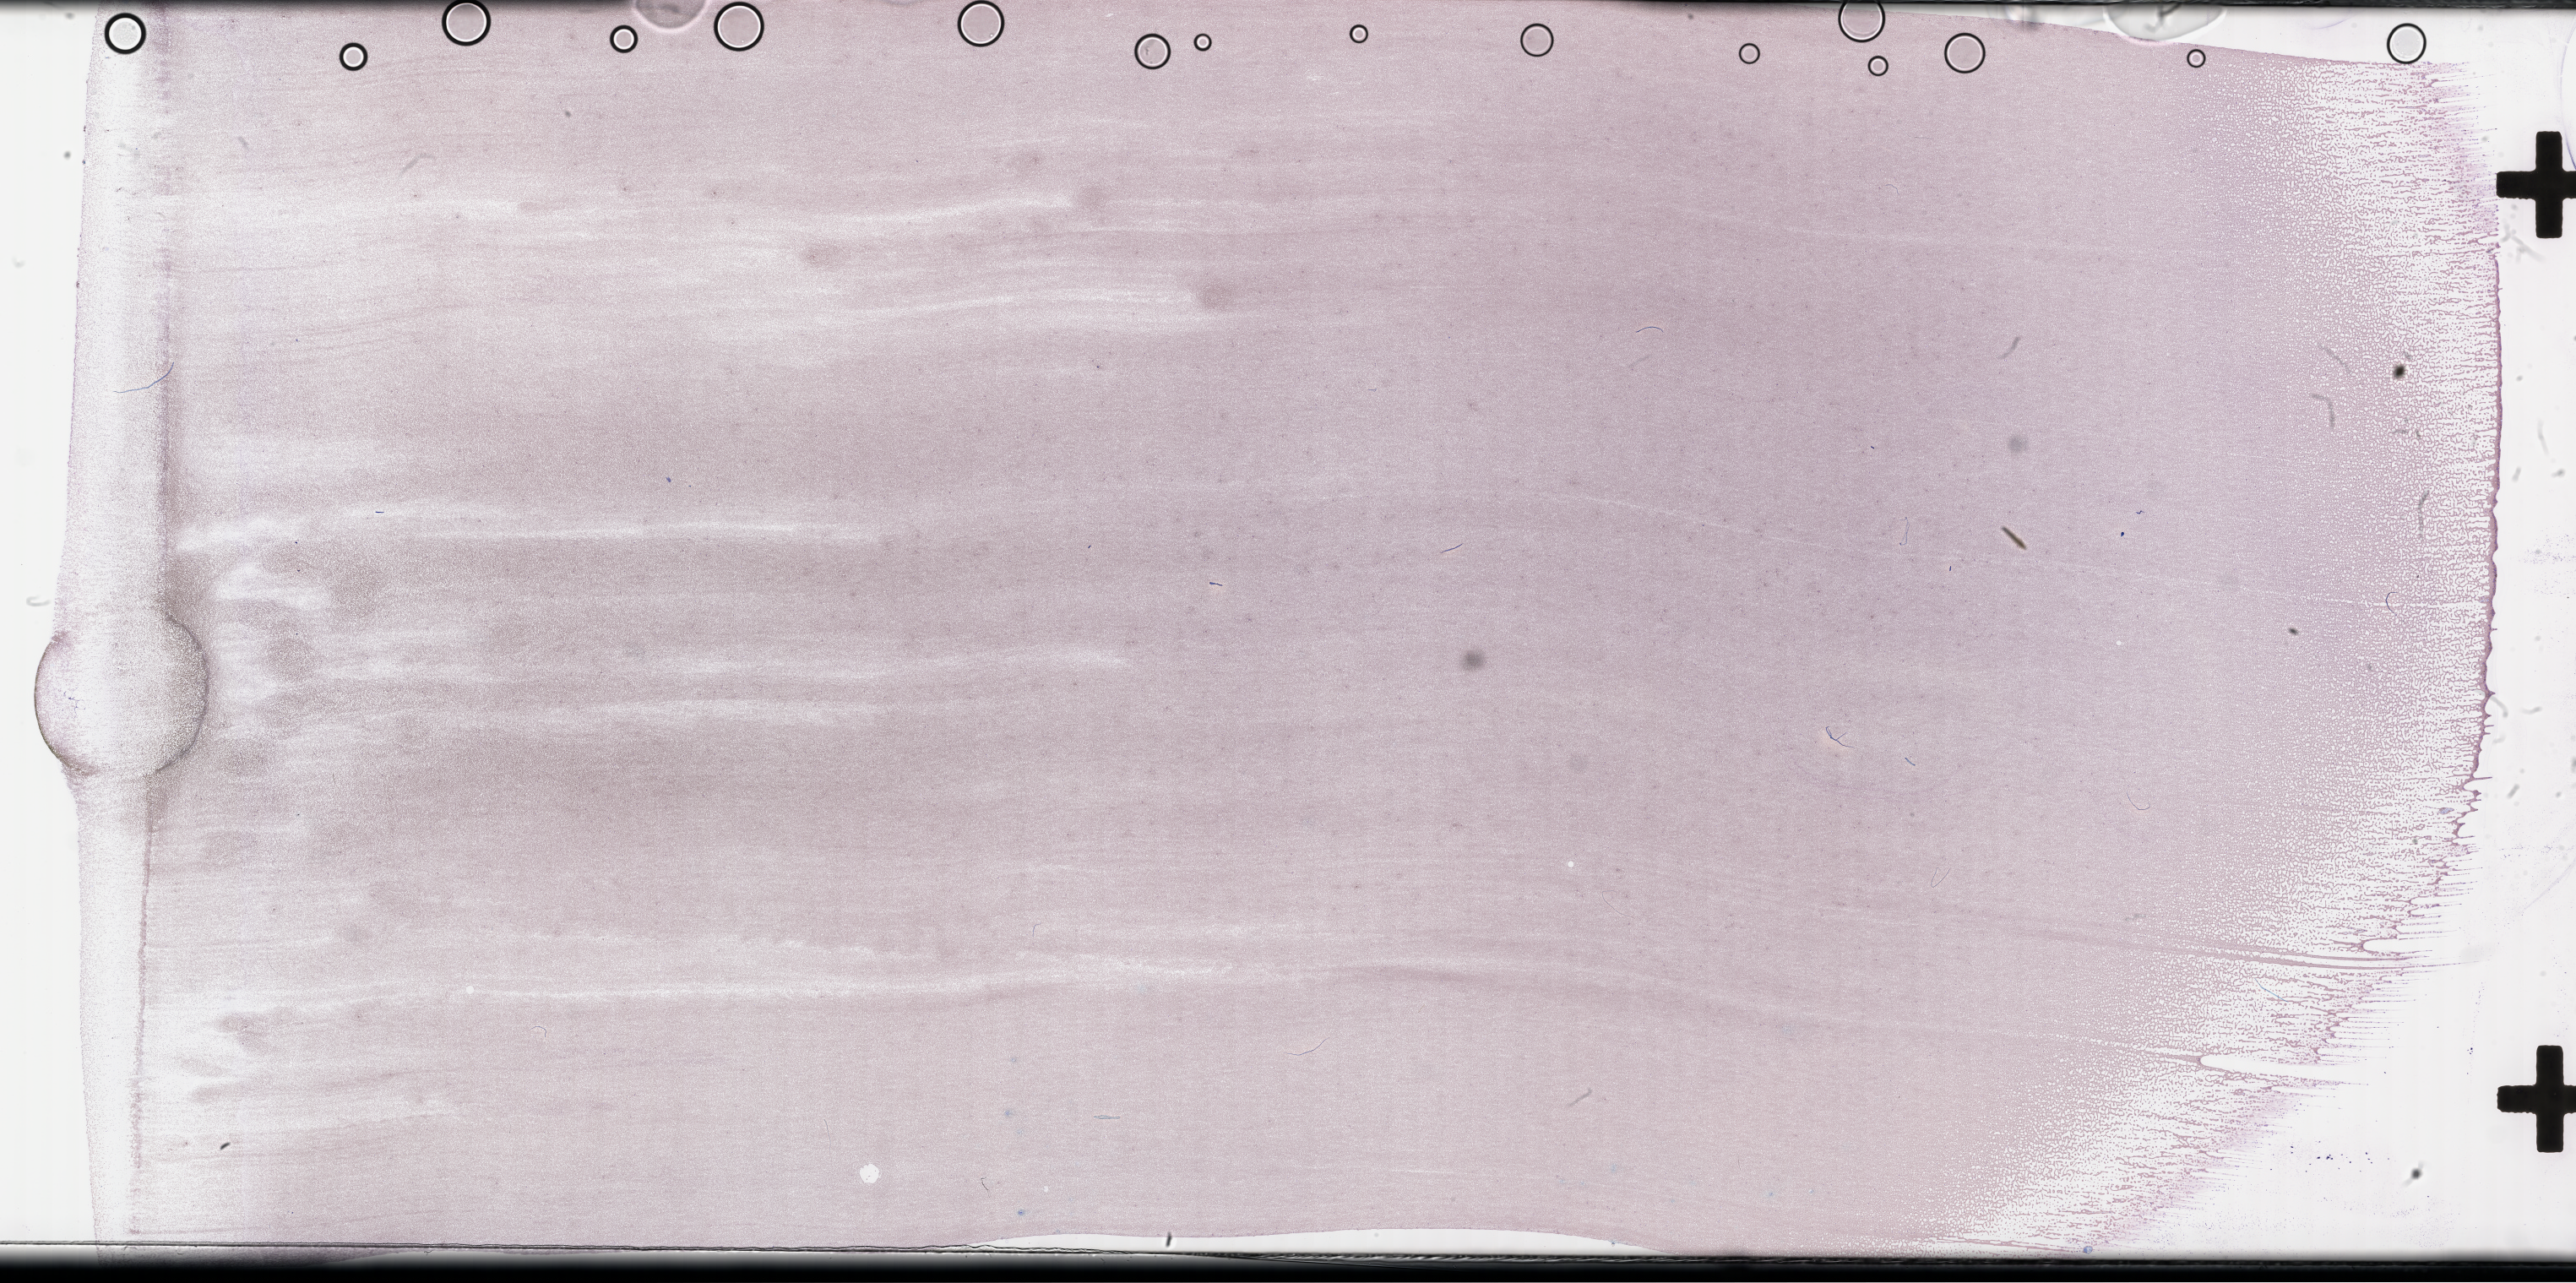
Whole-slide image of a whole blood smear, Wright-Giemsa stain, shown as a low-resolution overview of the whole scanned area (about 49.3 x 24.5 mm). EDTA-anticoagulated smear. Specimen time point: collected on treatment. Male patient.
From a patient with: Plasma Cell Myeloma.